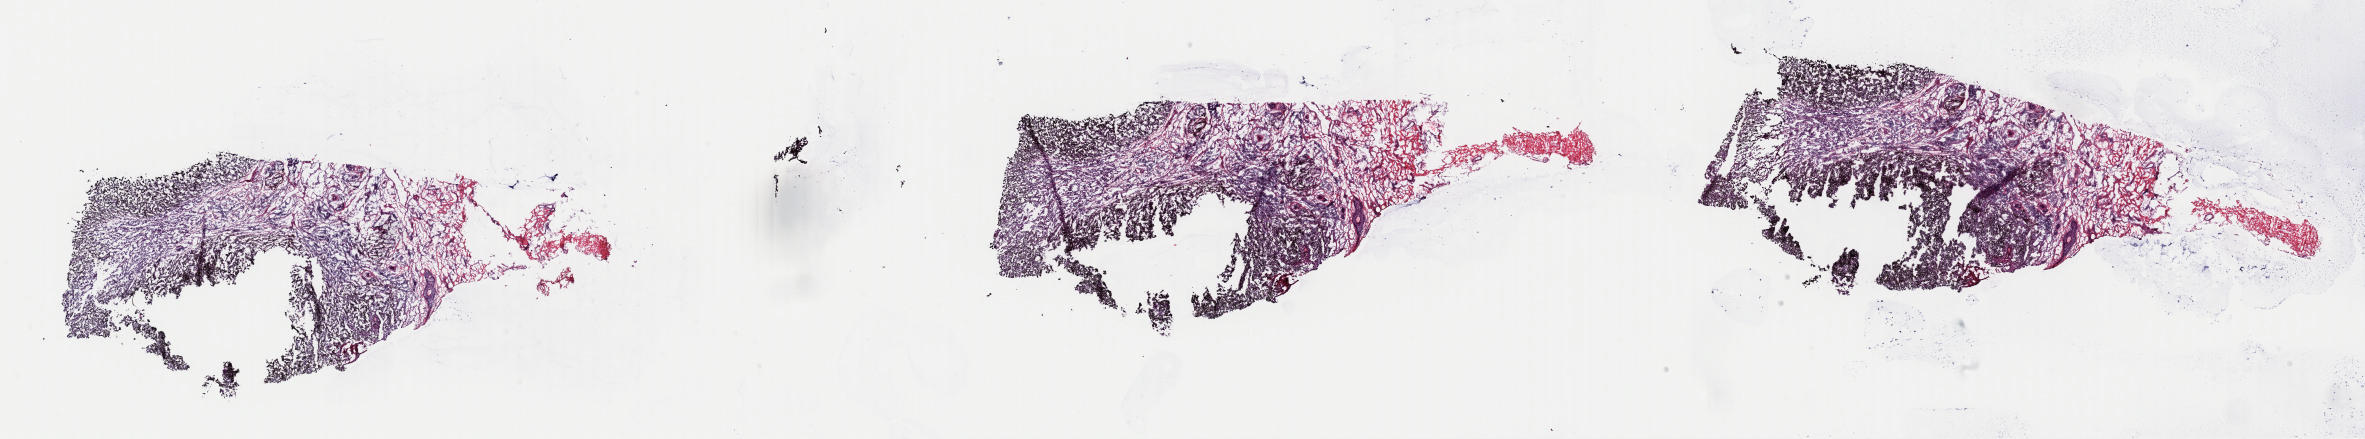
H&E-stained whole-slide image, a low-resolution overview of the entire scanned area, about 37.4 x 6.9 mm (acquisition: 40x scan). Frozen section. Skin, primary tumour sample. Patient: female, age at initial diagnosis 86 years. Composition of this section per pathologist review: tumour cells 65%, tumour nuclei 65%, normal cells 30%, stromal cells 5%, necrosis 0%. Inflammatory infiltration, as recorded: lymphocyte infiltration 0%, monocyte infiltration 0%, neutrophil infiltration 0%.
* AJCC pathologic stage: IIIB (7th edition)
* histologic diagnosis: Malignant melanoma, NOS